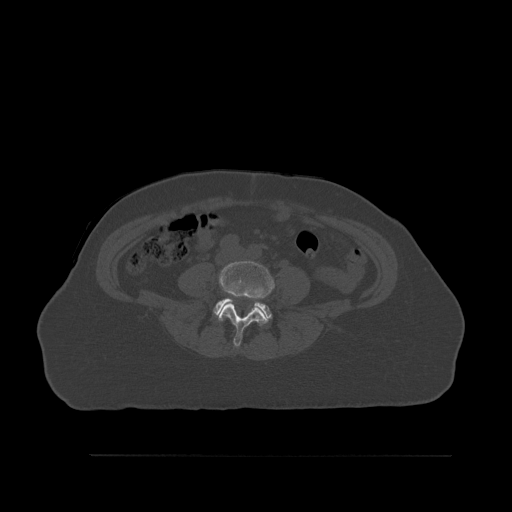
CT including the spine, one axial slice; slice 201 of 527 in the series (ordered by position); bone window (W 1800 / L 400 HU); 1.5 mm slice thickness; 512 × 512 image matrix, field of view 470 × 470 mm. Female patient, age 73 years. From the clinical record (not read from this slice): primary cancer: breast; vertebrae with lytic lesions (as recorded): L2.
Structures marked on this image (semi-automatically segmented with operator editing):
- L4 vertebra: bounding box (x1, y1, x2, y2) in pixels: (218, 261, 274, 347)
- L5 vertebra: (213, 298, 272, 325)